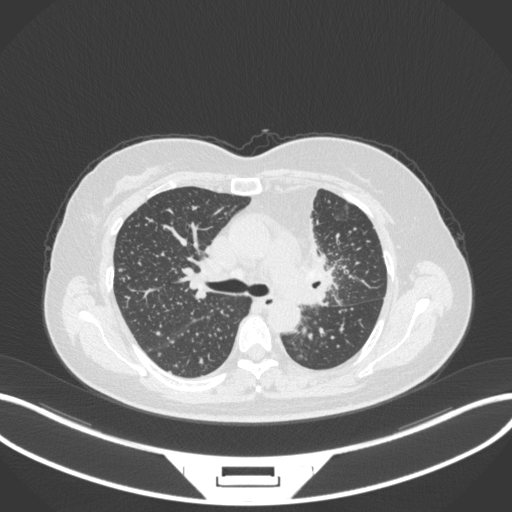
Chest CT, one axial slice; position 213 of 348 along the scan axis; reconstruction kernel B31f; 120 kVp; lung window (W 1500 / L -600 HU); 1 mm slice thickness; 512 × 512 image matrix. Female patient, age 49 years. From the clinical record (not read from this slice): clinical TNM (as recorded): T1c N0 M1.
Annotated regions visible in this slice (bounding box drawn by a radiologist):
- lung tumour (recorded histology: adenocarcinoma): box from (x=295, y=219) to (x=335, y=307) px